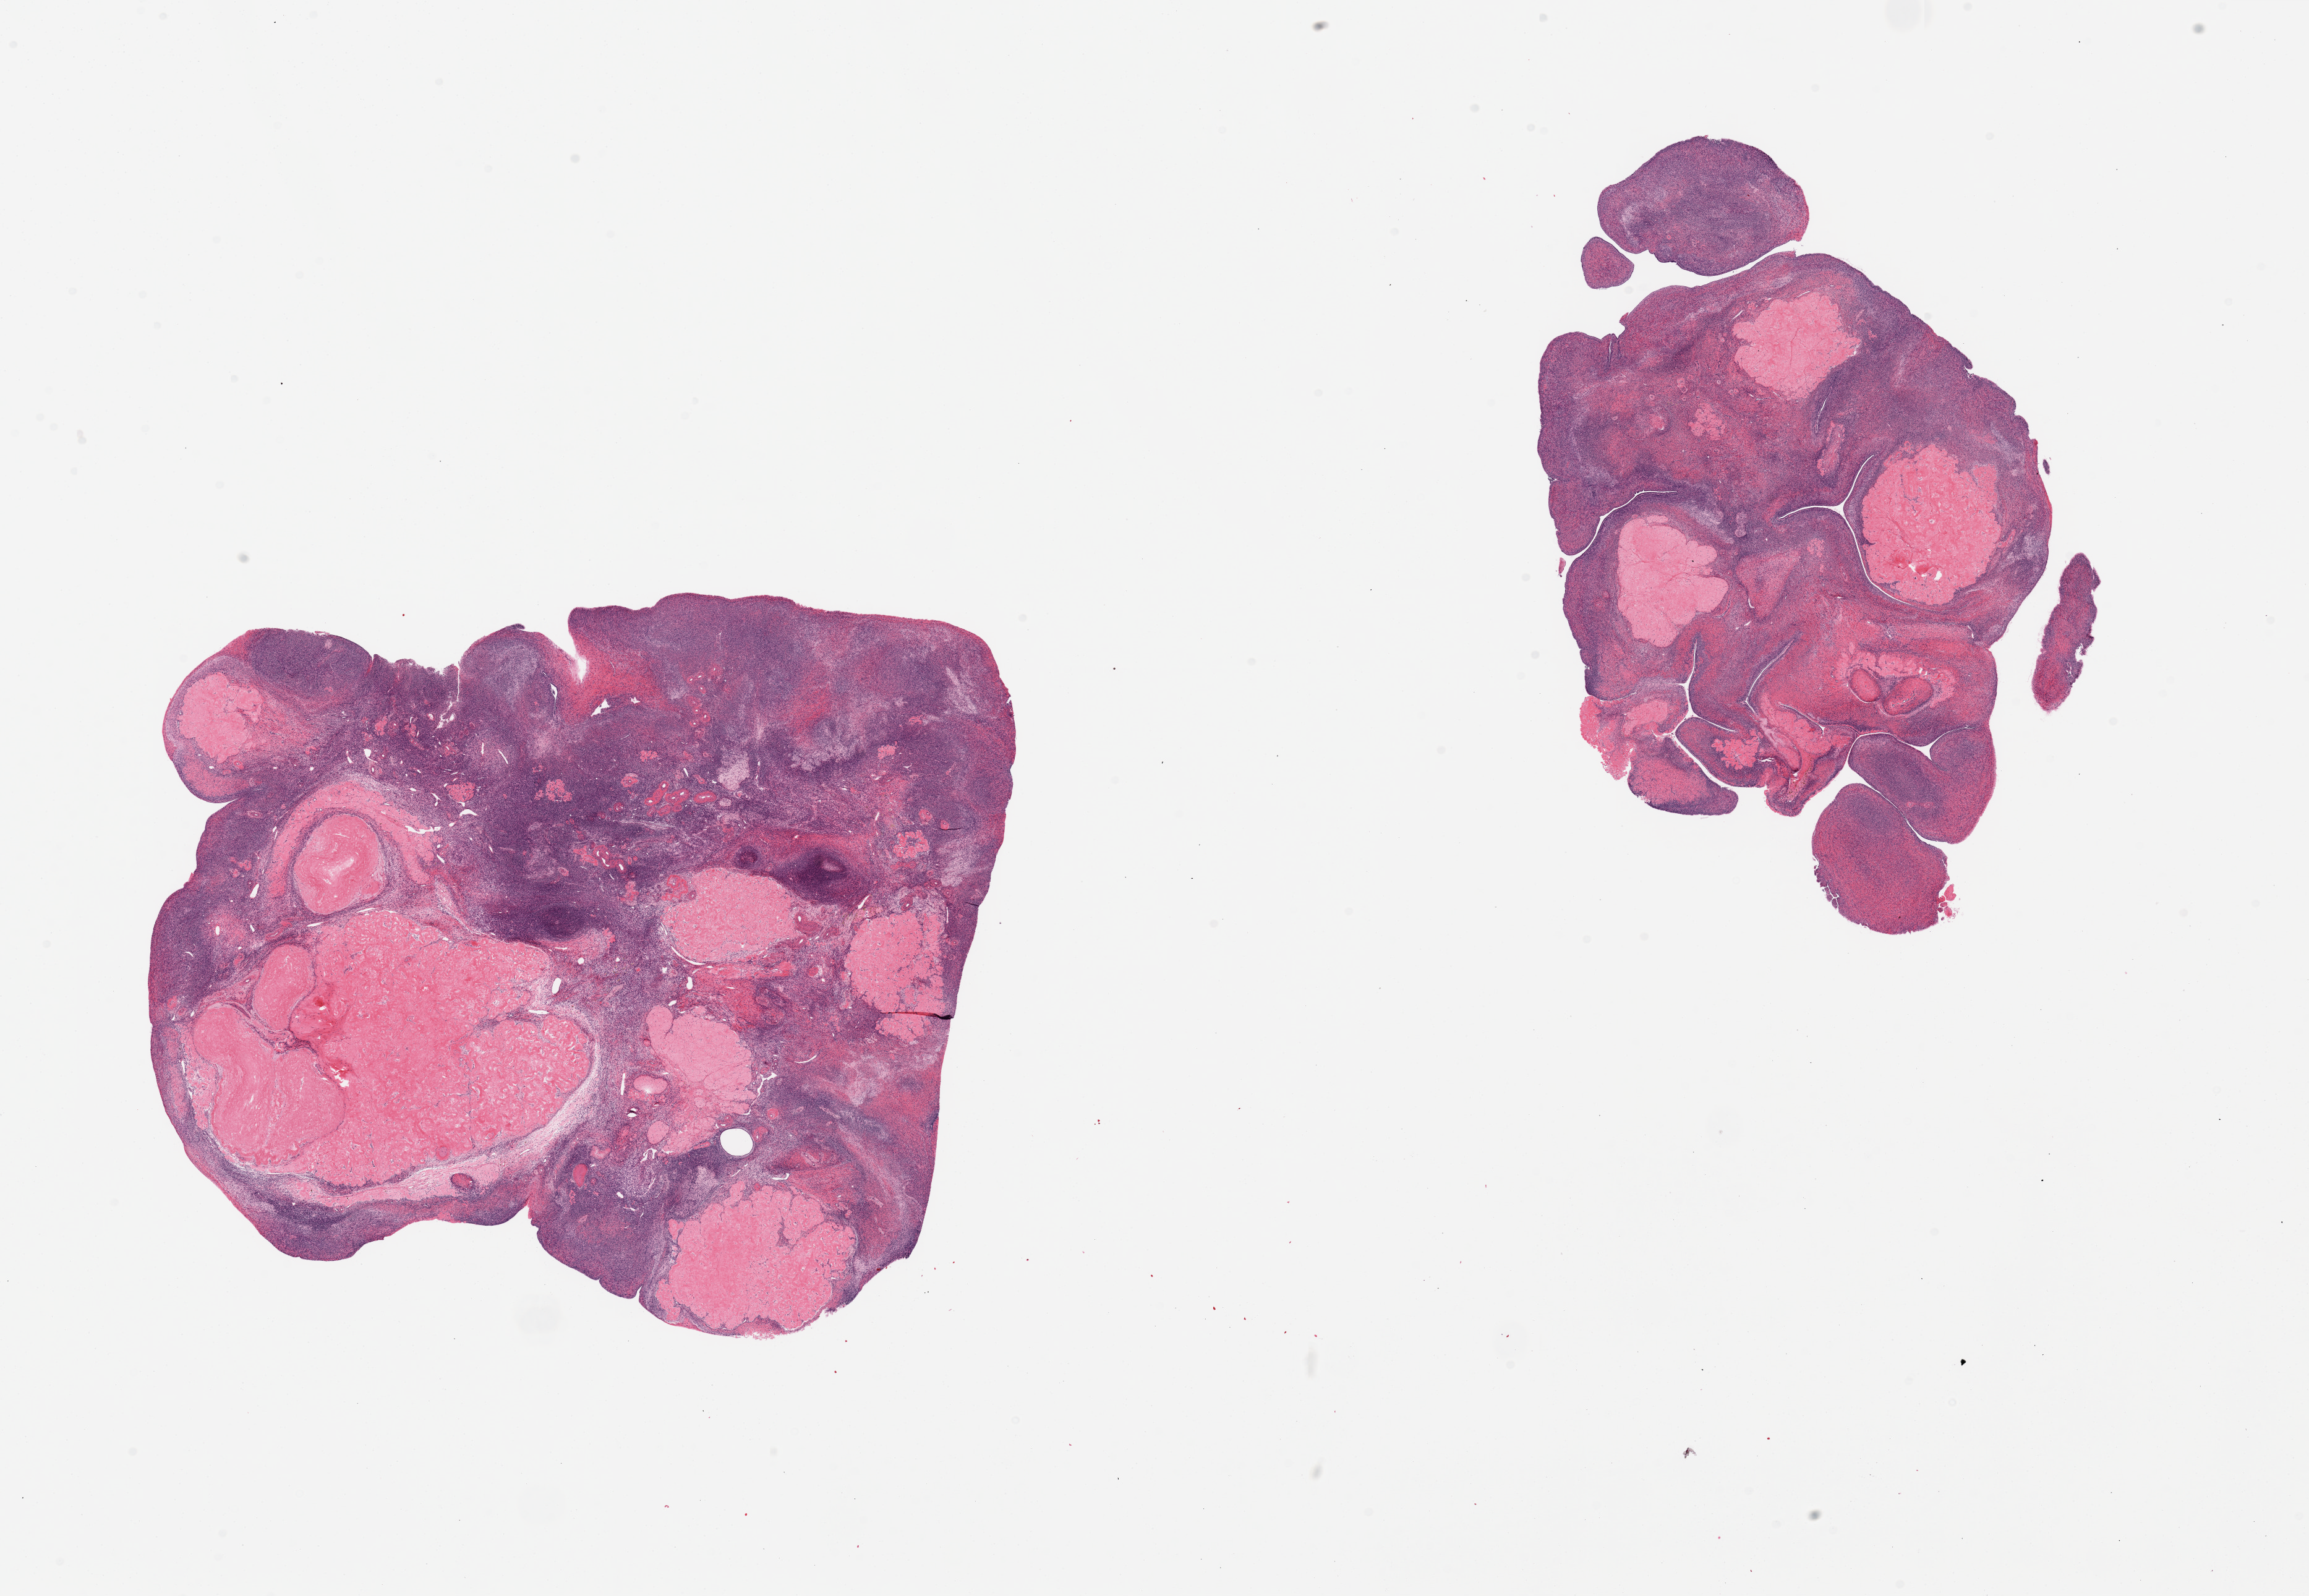
Digitized H&E-stained section — shown as a low-resolution overview of the whole scanned area (about 29.5 x 20.4 mm, from a 20x scan). PAXgene-fixed paraffin-embedded (PFPE) section. Sampled site (target tissue): ovary. Donor tissue sample. Donor: female.
Pathologist's review note for this sample: 2 pieces; numerous corpora albicans comprise 50 and 25% of samples.